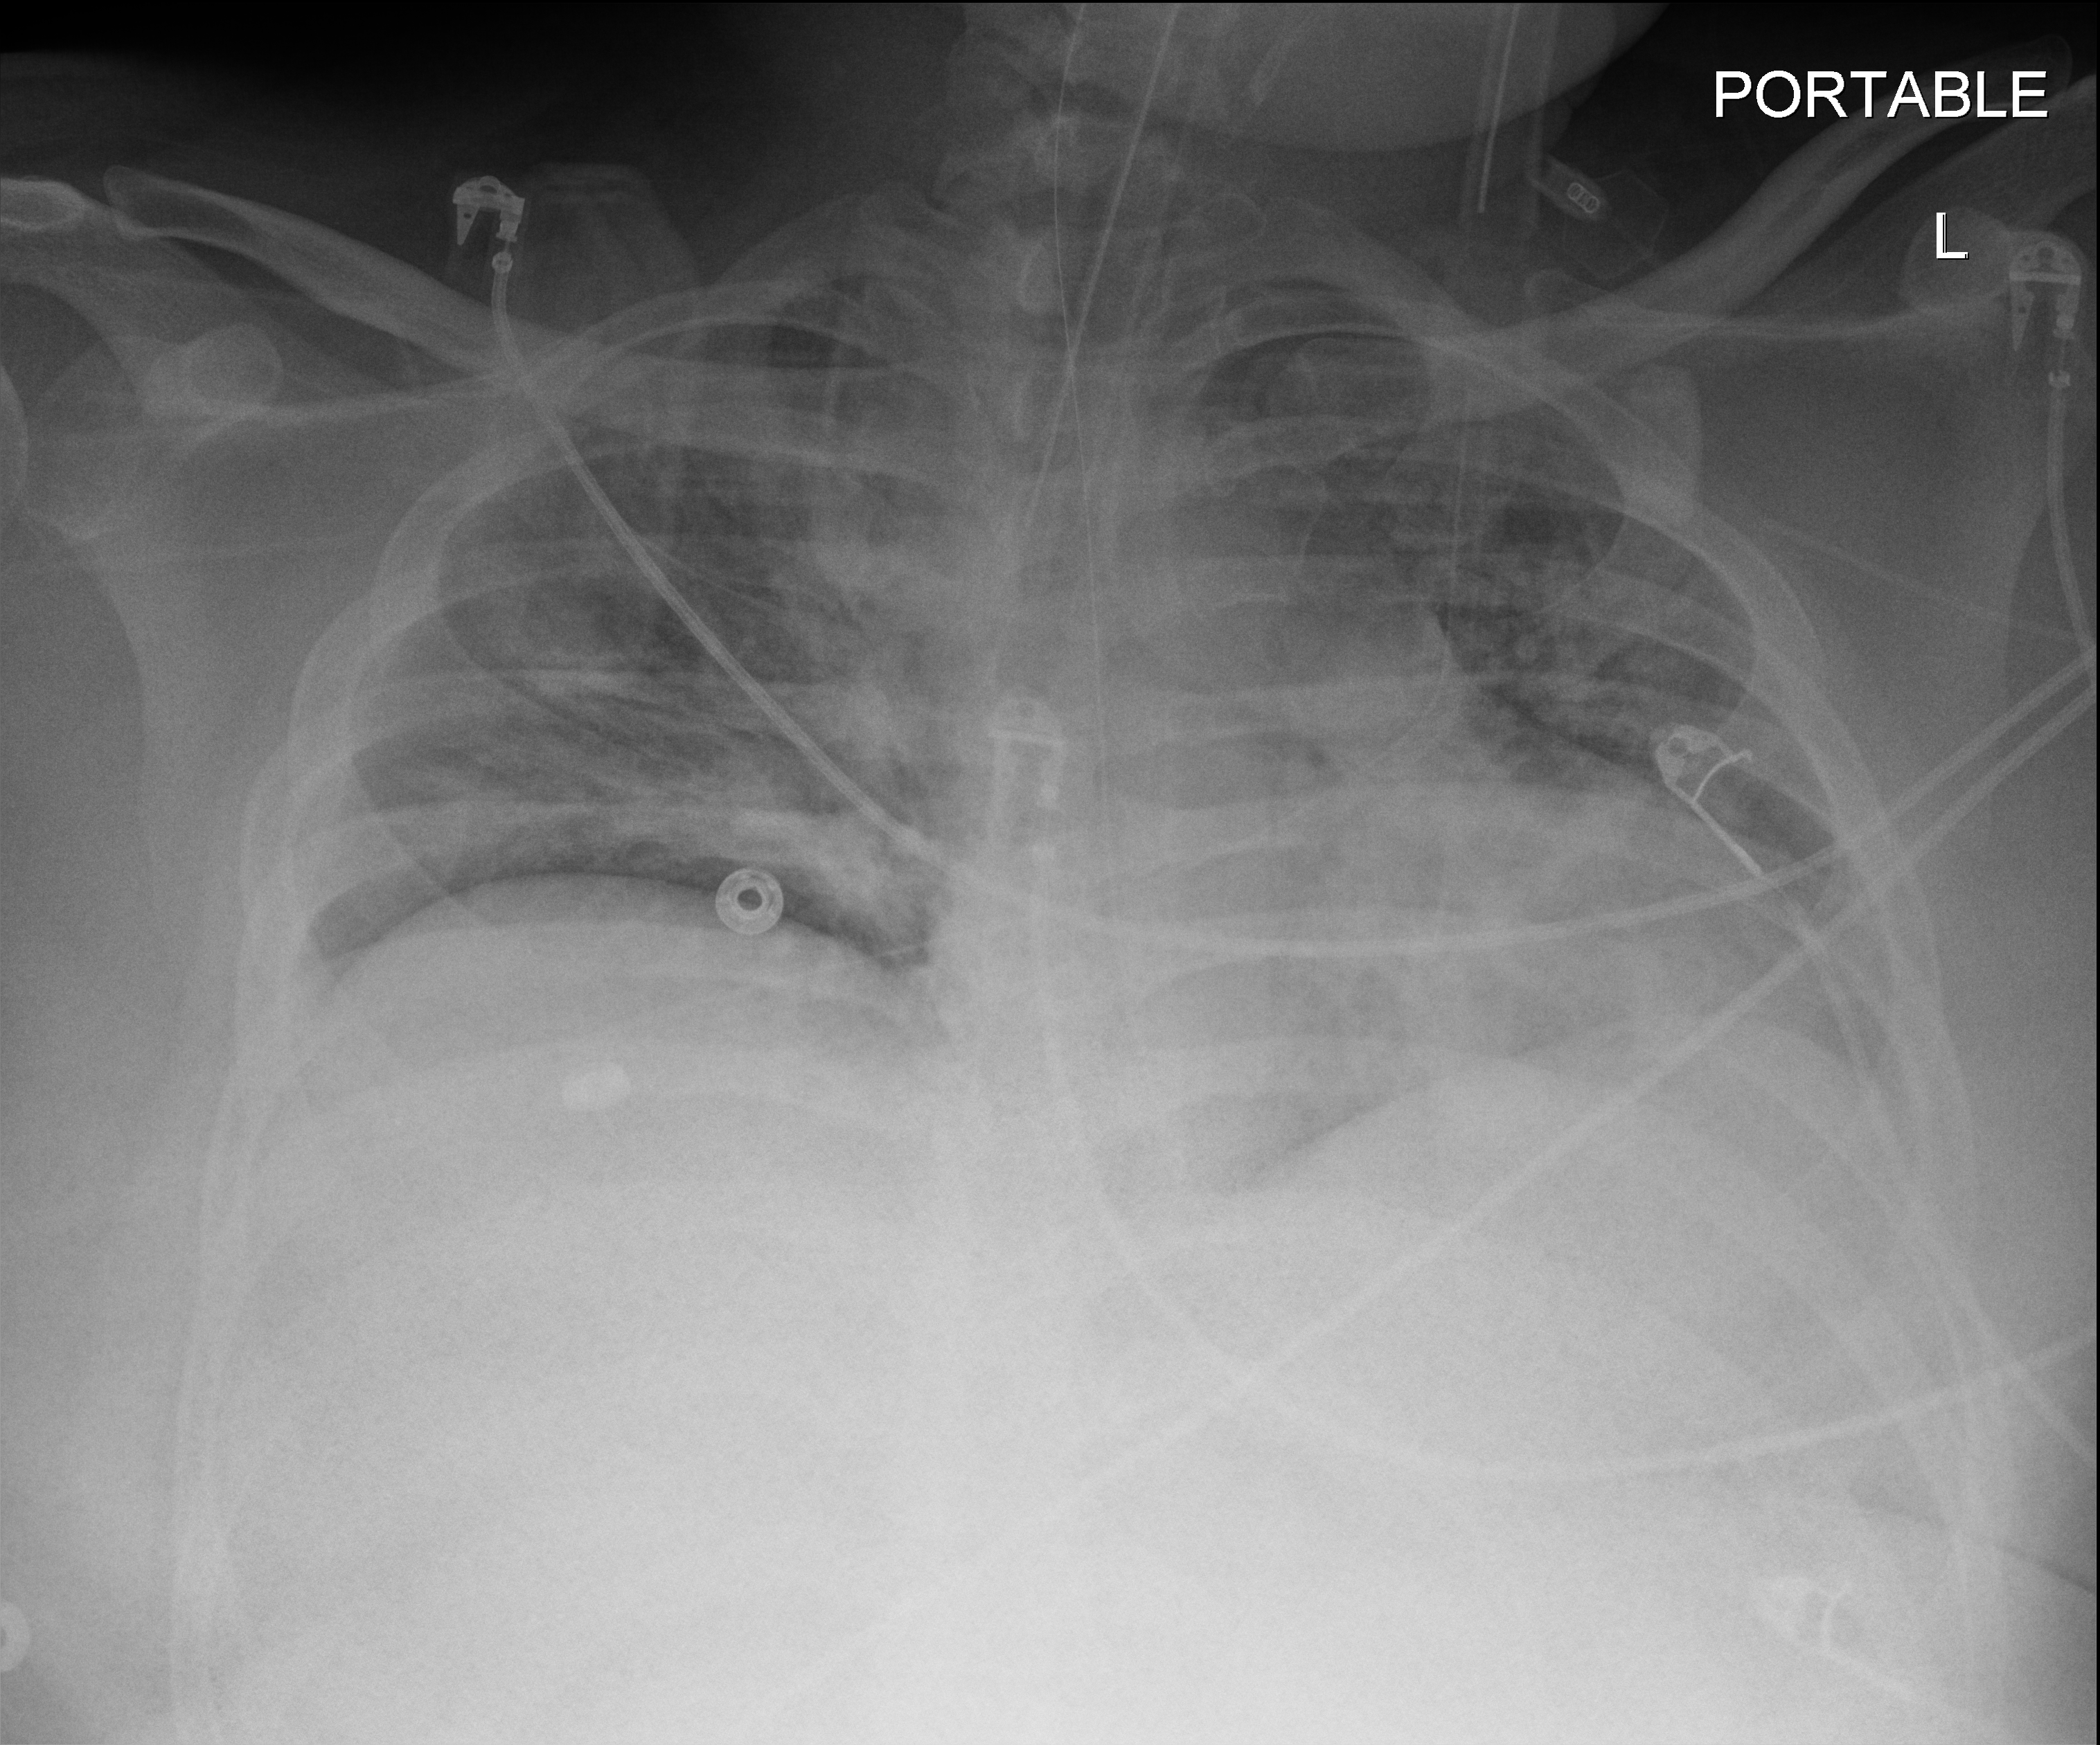
Bedside chest radiograph (digital radiography); anteroposterior (AP) projection. Patient hospitalised with COVID-19; male, aged 18–59 years.
Admission-level facts for this patient (not findings on this image; timing relative to this image not recorded): mechanically ventilated during this hospital stay: yes.